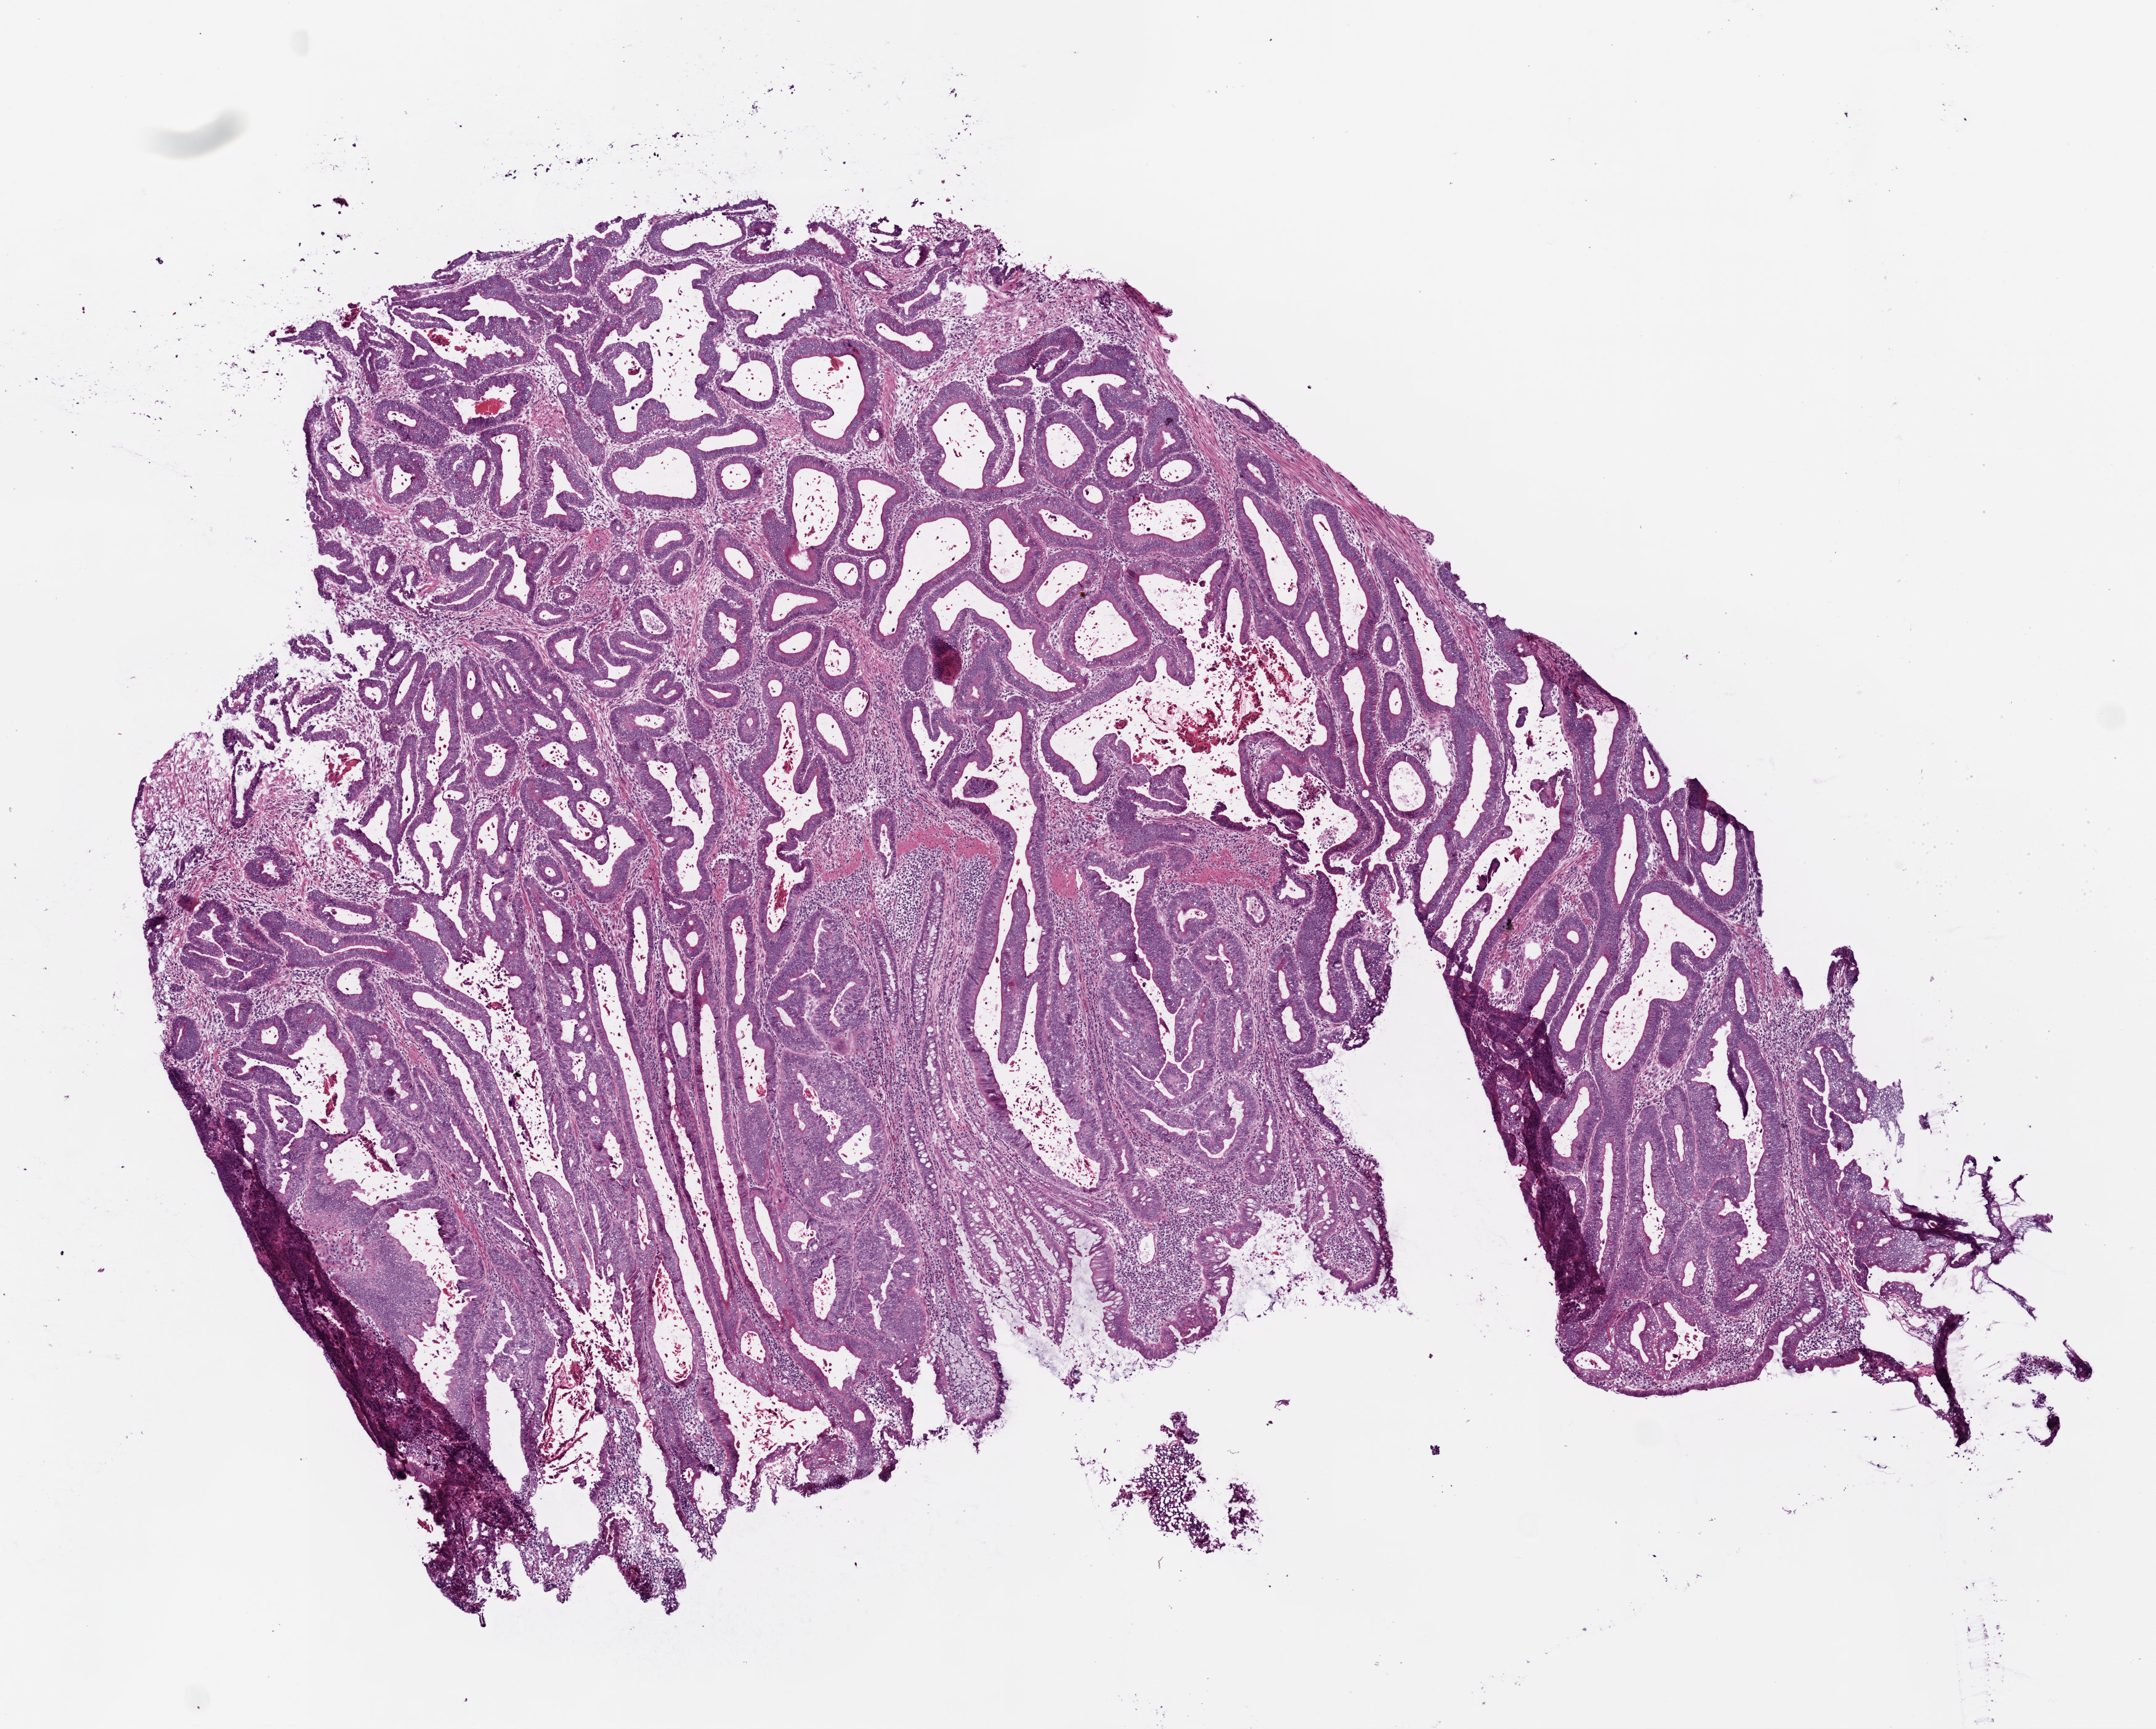
Whole-slide histology image, H&E-stained, low-resolution overview of the scanned area, about 7.0 x 5.6 mm, frozen section from the bottom of the tissue portion, colon, primary tumour sample. Female patient; age at initial diagnosis 63 years. Composition of this section per pathologist review: tumour cells 72%, tumour nuclei 70%, normal cells 10%, stromal cells 10%, necrosis 8%.
Lymph nodes positive (case pathology): 0 of 25 examined. Histologic diagnosis: Adenocarcinoma, NOS (sigmoid colon). AJCC pathologic stage: I (6th edition).